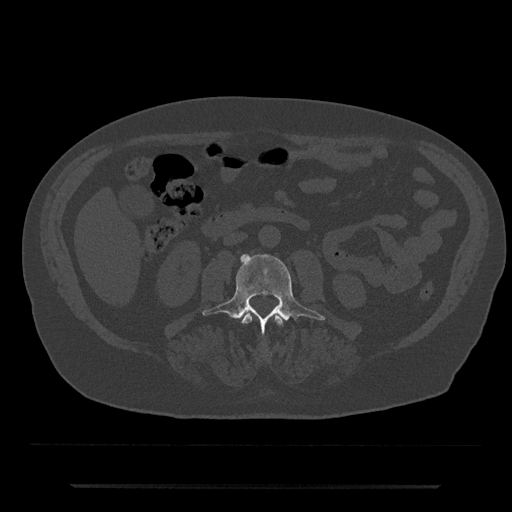
CT including the spine, one axial slice; position 419 of 797 along the scan axis; 120 kVp; bone window (W 1800 / L 400 HU); 0.5 mm slice thickness; 512 × 512 image matrix, field of view 434 × 434 mm. Patient: male, 80 years. Case-level facts recorded for this patient, not image findings: primary cancer: prostate; vertebrae with lytic lesions (as recorded): L1, T11.
Structures marked on this image (semi-automatically segmented with operator editing):
- L2 vertebra: bounding box (x1, y1, x2, y2) in pixels: (242, 314, 282, 325)
- L3 vertebra: (202, 254, 325, 336)